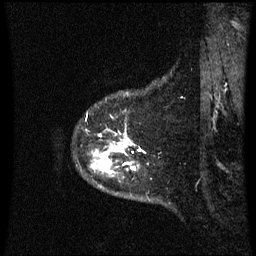
Breast MRI (dynamic contrast-enhanced), one sagittal slice. Position 55 of 60 along the scan axis. Dynamic contrast-enhanced series, image 2 of 3 at this slice position (ordered by acquisition). 1.5 T. TE 4.2 ms, TR 8.9 ms. 2.3 mm slice thickness. 256 × 256 image matrix, field of view 210 × 210 mm. Patient: female, 43 years. From the clinical record (not read from this slice): setting: breast cancer imaged before/during neoadjuvant chemotherapy; receptor status: HER2-positive.
Structures marked on this image (semi-automatically segmented with operator editing):
- analysis volume of interest (the breast-tissue region the enhancement analysis was run in; not a lesion): bounding box (x1, y1, x2, y2) in pixels: (87, 114, 146, 179)
- tumour enhancement mask (voxels above the 70 % enhancement threshold inside the analysis volume of interest): (94, 135, 142, 172)